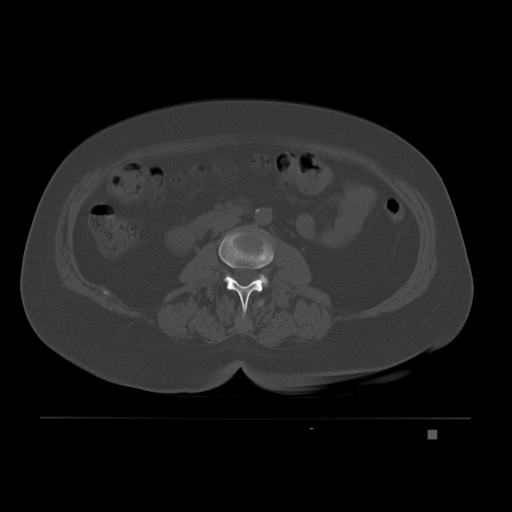
CT including the spine, one axial slice. Slice 59 of 221 in the series (ordered by position). Bone window (W 1800 / L 400 HU). 3 mm slice thickness. 512 × 512 image matrix. Patient: female, 63 years. Case-level facts recorded for this patient, not image findings: primary cancer: breast.
Outlined on this slice (semi-automatic segmentation, software-assisted and operator-edited):
- L2 vertebra: bounding box <218,230,274,318> (left, top, right, bottom; pixels)
- L3 vertebra: <225,274,268,288>